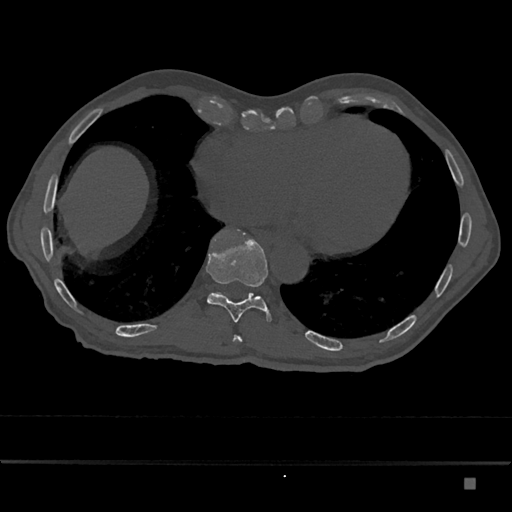
CT including the spine, one axial slice. Slice 736 of 797 in the series (ordered by position). Bone window (W 1800 / L 400 HU). 0.5 mm slice thickness. 512 × 512 image matrix. Male patient, age 72 years. From the clinical record (not read from this slice): primary cancer: prostate.
Structures marked on this image (semi-automatically segmented with operator editing):
- T10 vertebra: box from (x=206, y=234) to (x=271, y=323) px
- T11 vertebra: (x=217, y=292)–(x=253, y=294)
- T9 vertebra: (x=234, y=335)–(x=242, y=342)